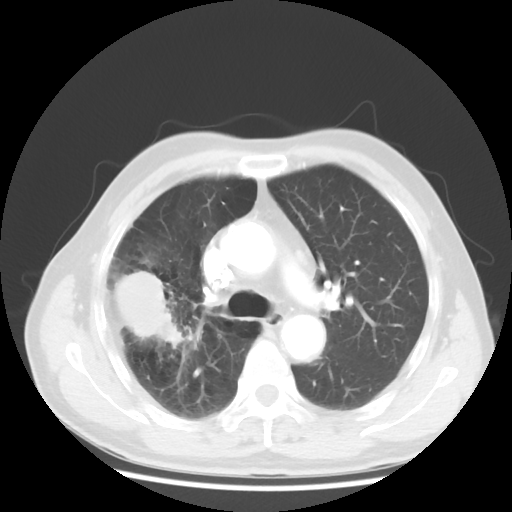
Chest CT, one axial slice. 120 kVp. Lung window (W 1500 / L -600 HU). 512 × 512 image matrix, field of view 360 × 360 mm. Male patient, age 69 years. Case-level facts recorded for this patient, not image findings: clinical TNM (as recorded): T3 N0 M0; histopathological grade: G3.
Outlined on this slice (bounding box drawn by a radiologist):
- lung tumour (recorded histology: adenocarcinoma): box from (x=108, y=268) to (x=188, y=351) px